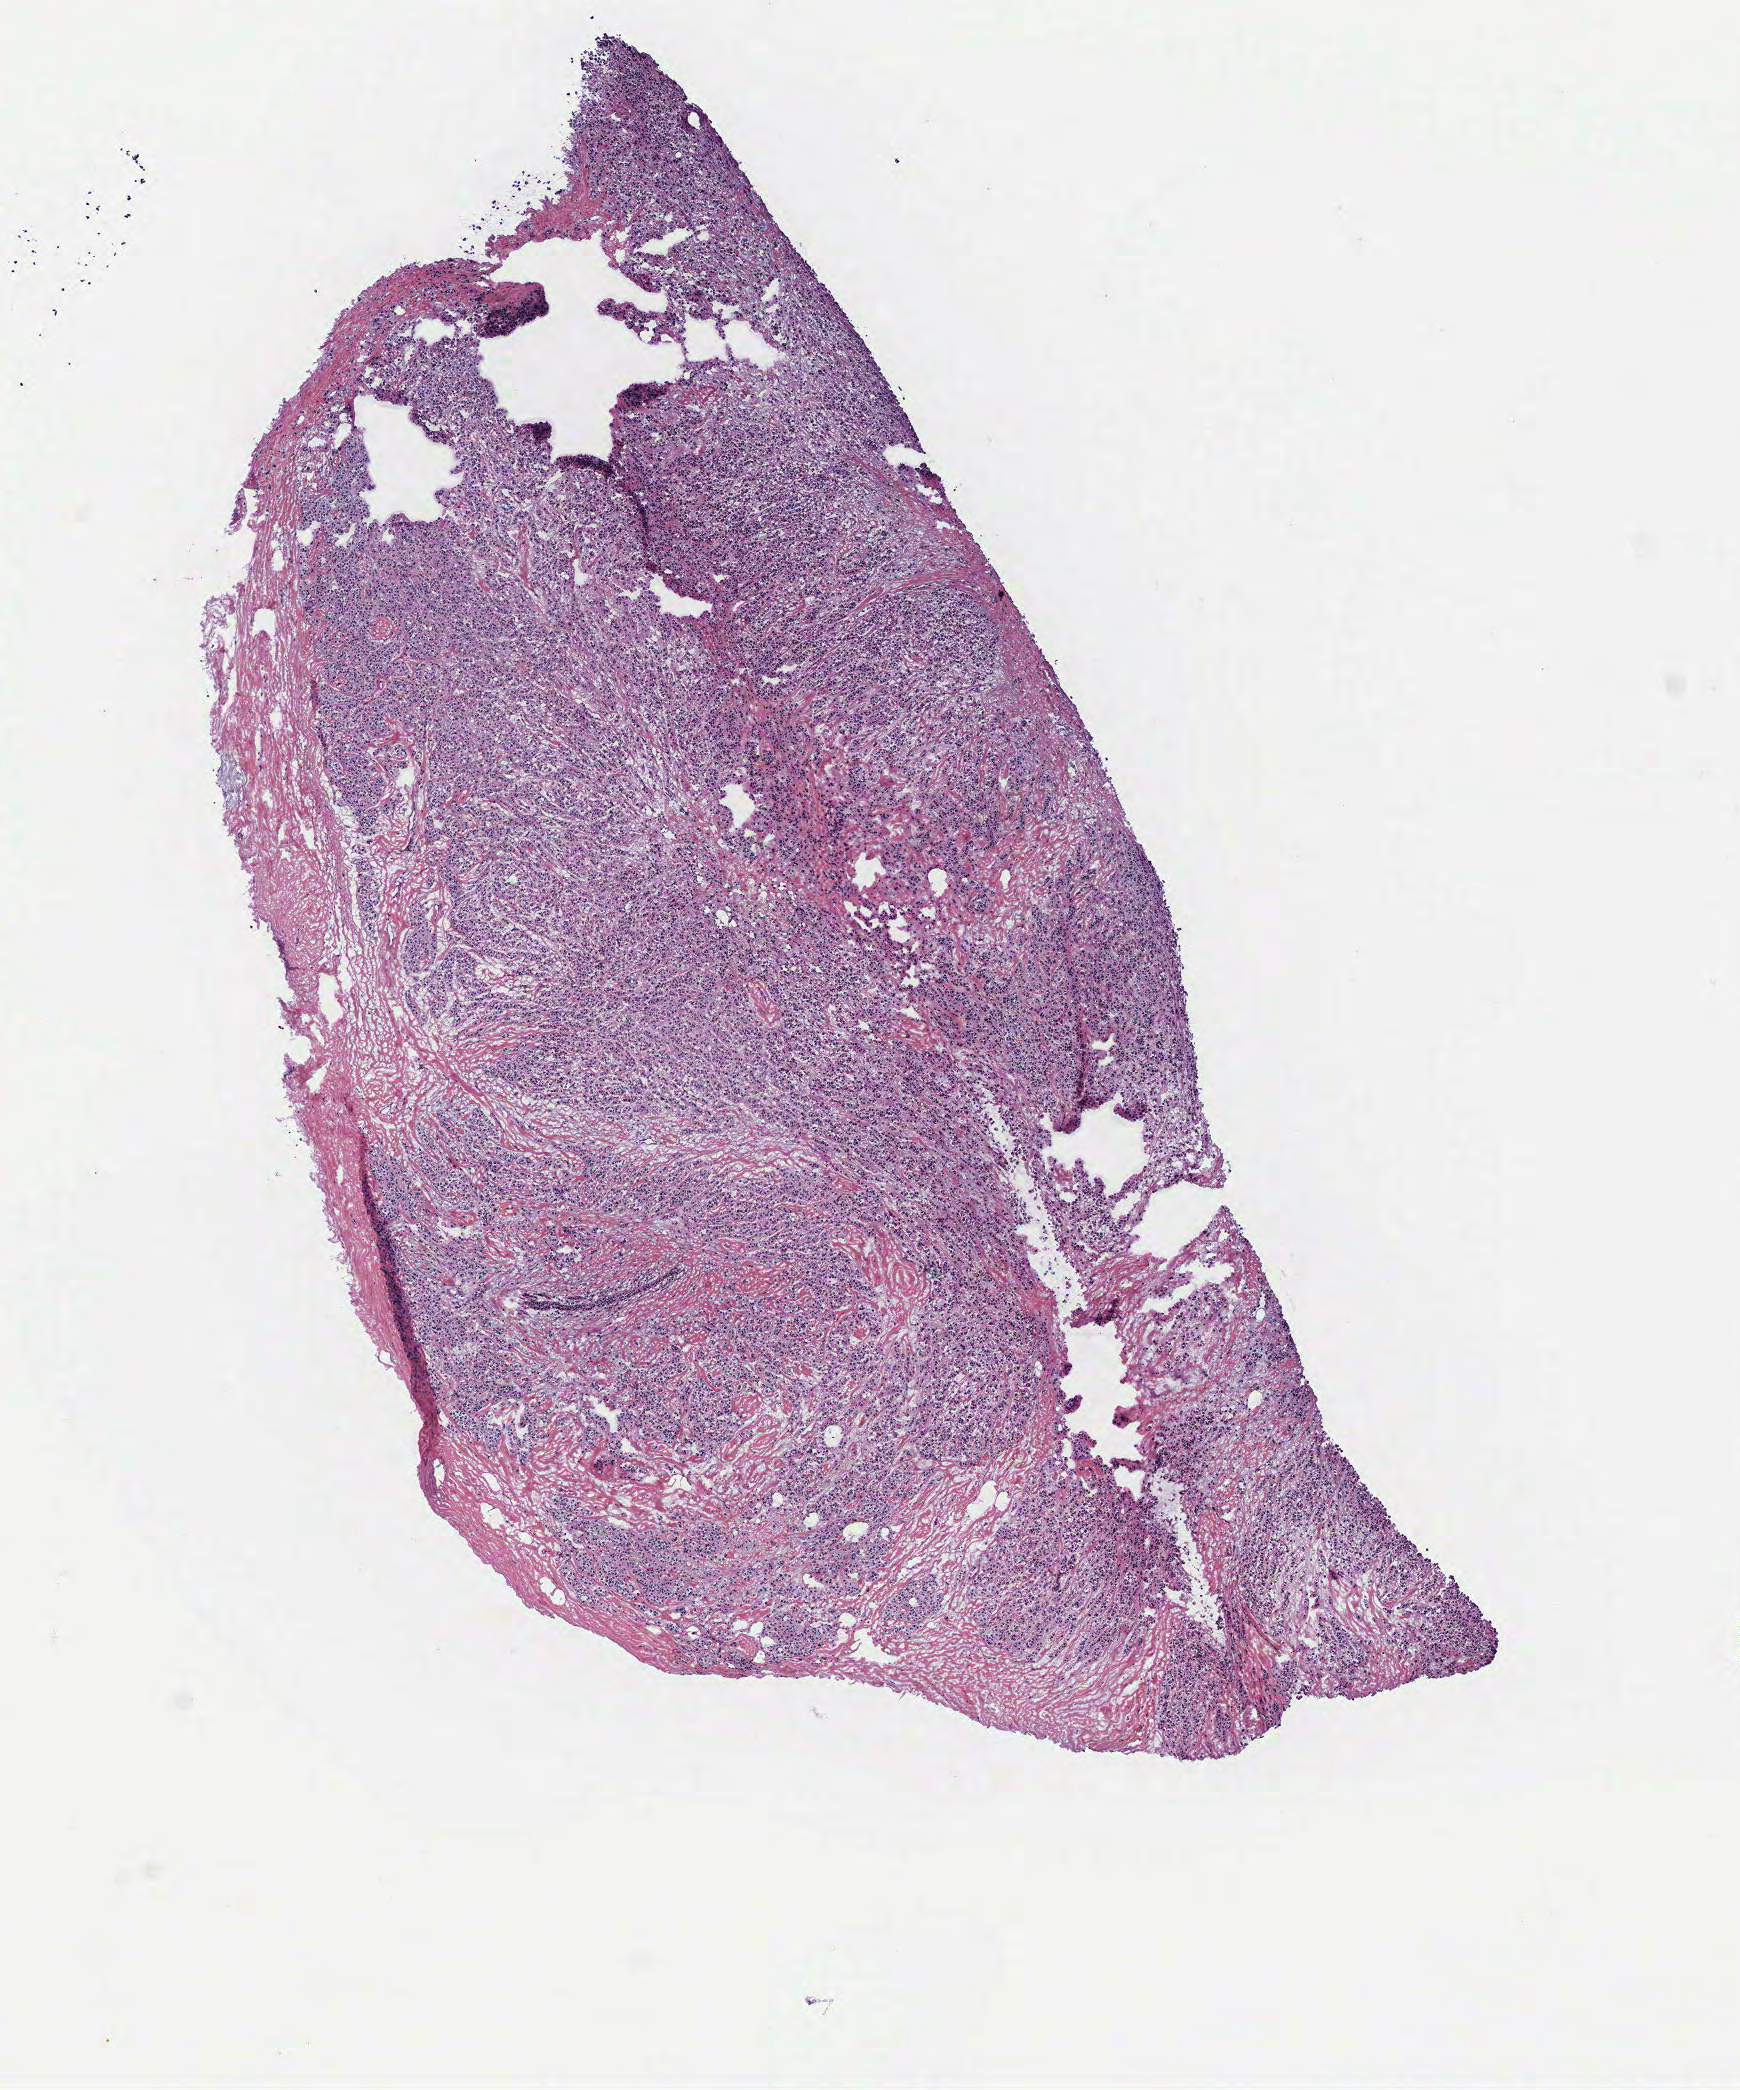
Whole-slide histology image, H&E-stained, low-resolution overview of the scanned area, about 7.0 x 8.4 mm, tumour tissue sample, breast. Female, 78 y/o.
• histologic diagnosis: Infiltrating lobular carcinoma, NOS
• AJCC pathologic stage: IIA